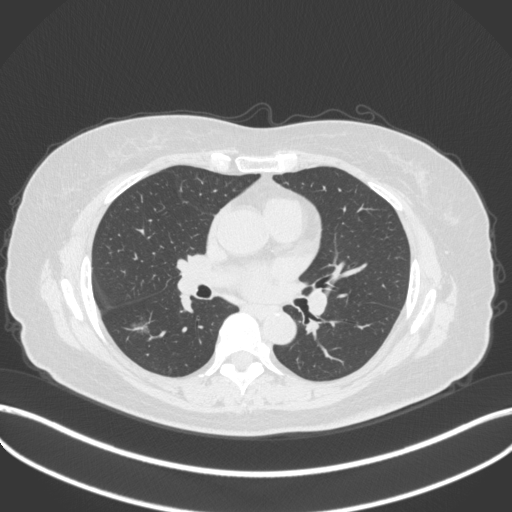
Chest CT, one axial slice; slice 168 of 322 in the series (ordered by position); reconstruction kernel B31f; 120 kVp; lung window (W 1500 / L -600 HU); 1 mm slice thickness; 512 × 512 image matrix, field of view 400 × 400 mm. Patient: female, 64 years. From the clinical record (not read from this slice): clinical TNM (as recorded): T1c N0 M0.
Annotated regions visible in this slice (rectangle marked by the reading radiologist):
- lung tumour (recorded histology: adenocarcinoma): bounding box [x1, y1, x2, y2] px = [121, 311, 162, 340]